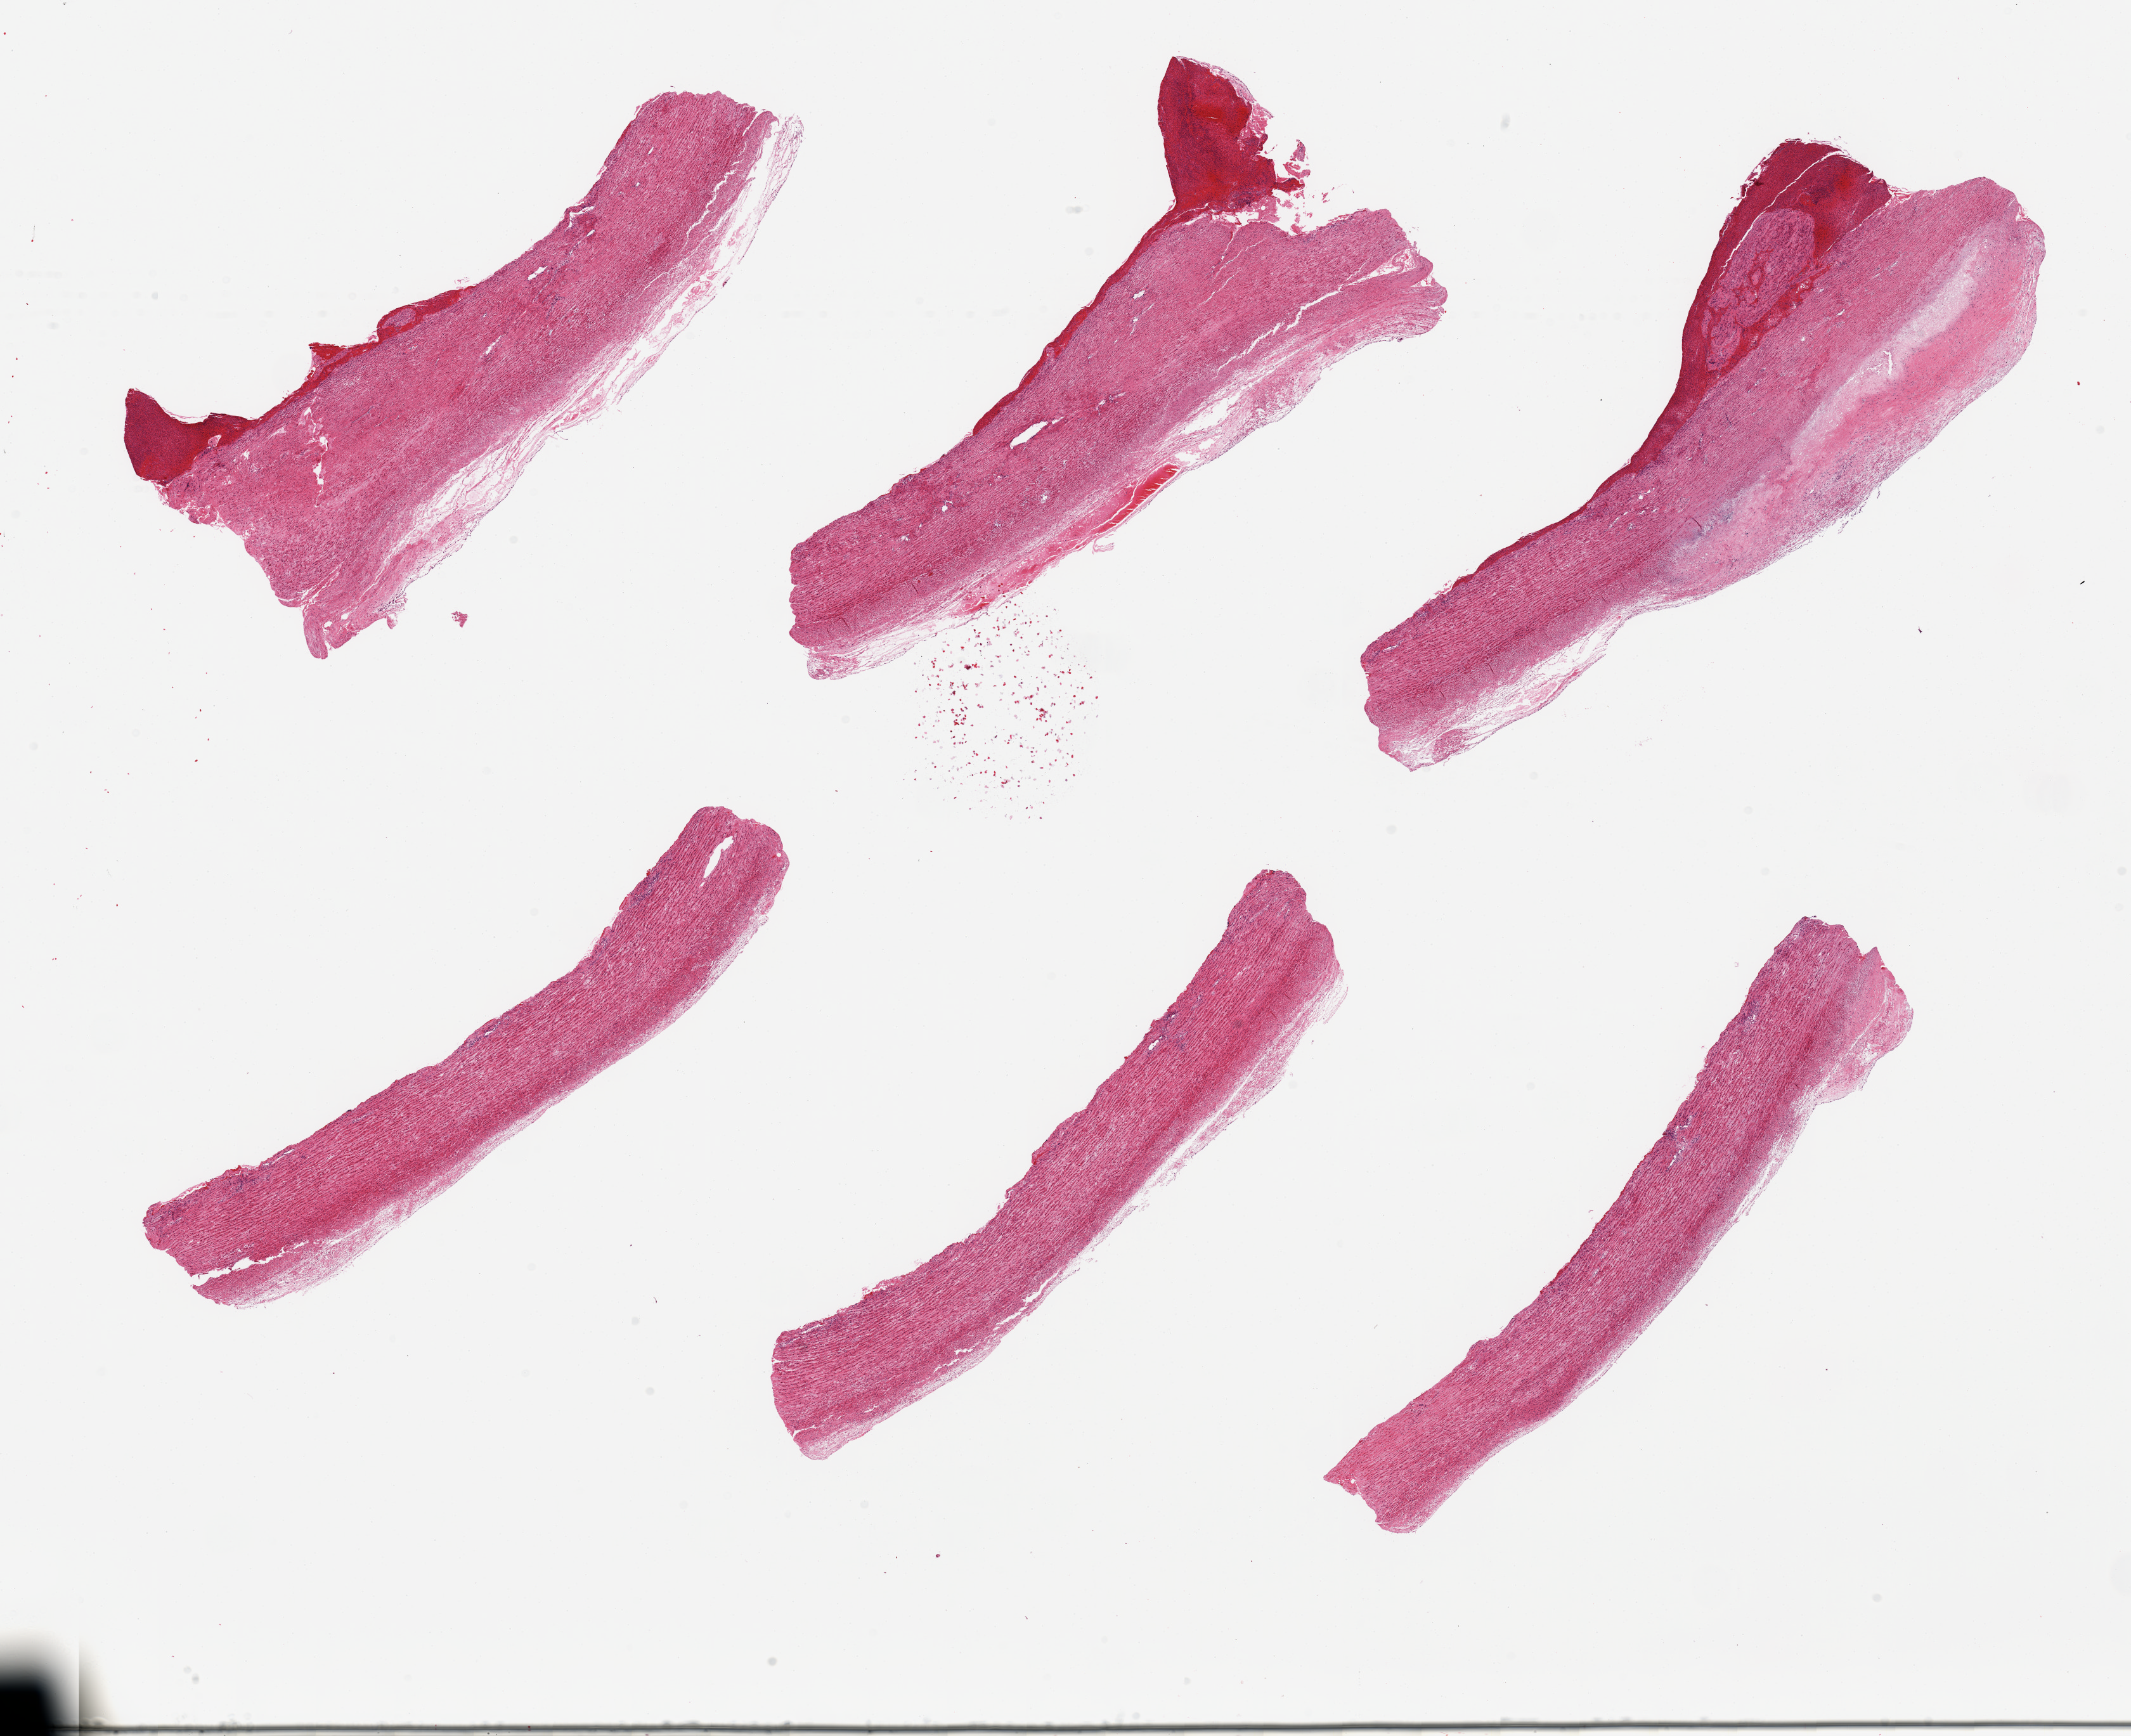
Whole-slide image, H&E stain, low-resolution overview of the scanned area, about 26.6 x 21.7 mm. PAXgene-fixed paraffin-embedded (PFPE) section. Target tissue: aorta. Tissue donor sample.
Pathologist's review note for this sample: 6 pieces, foci of atherosis, up to 1.5 mm thick.